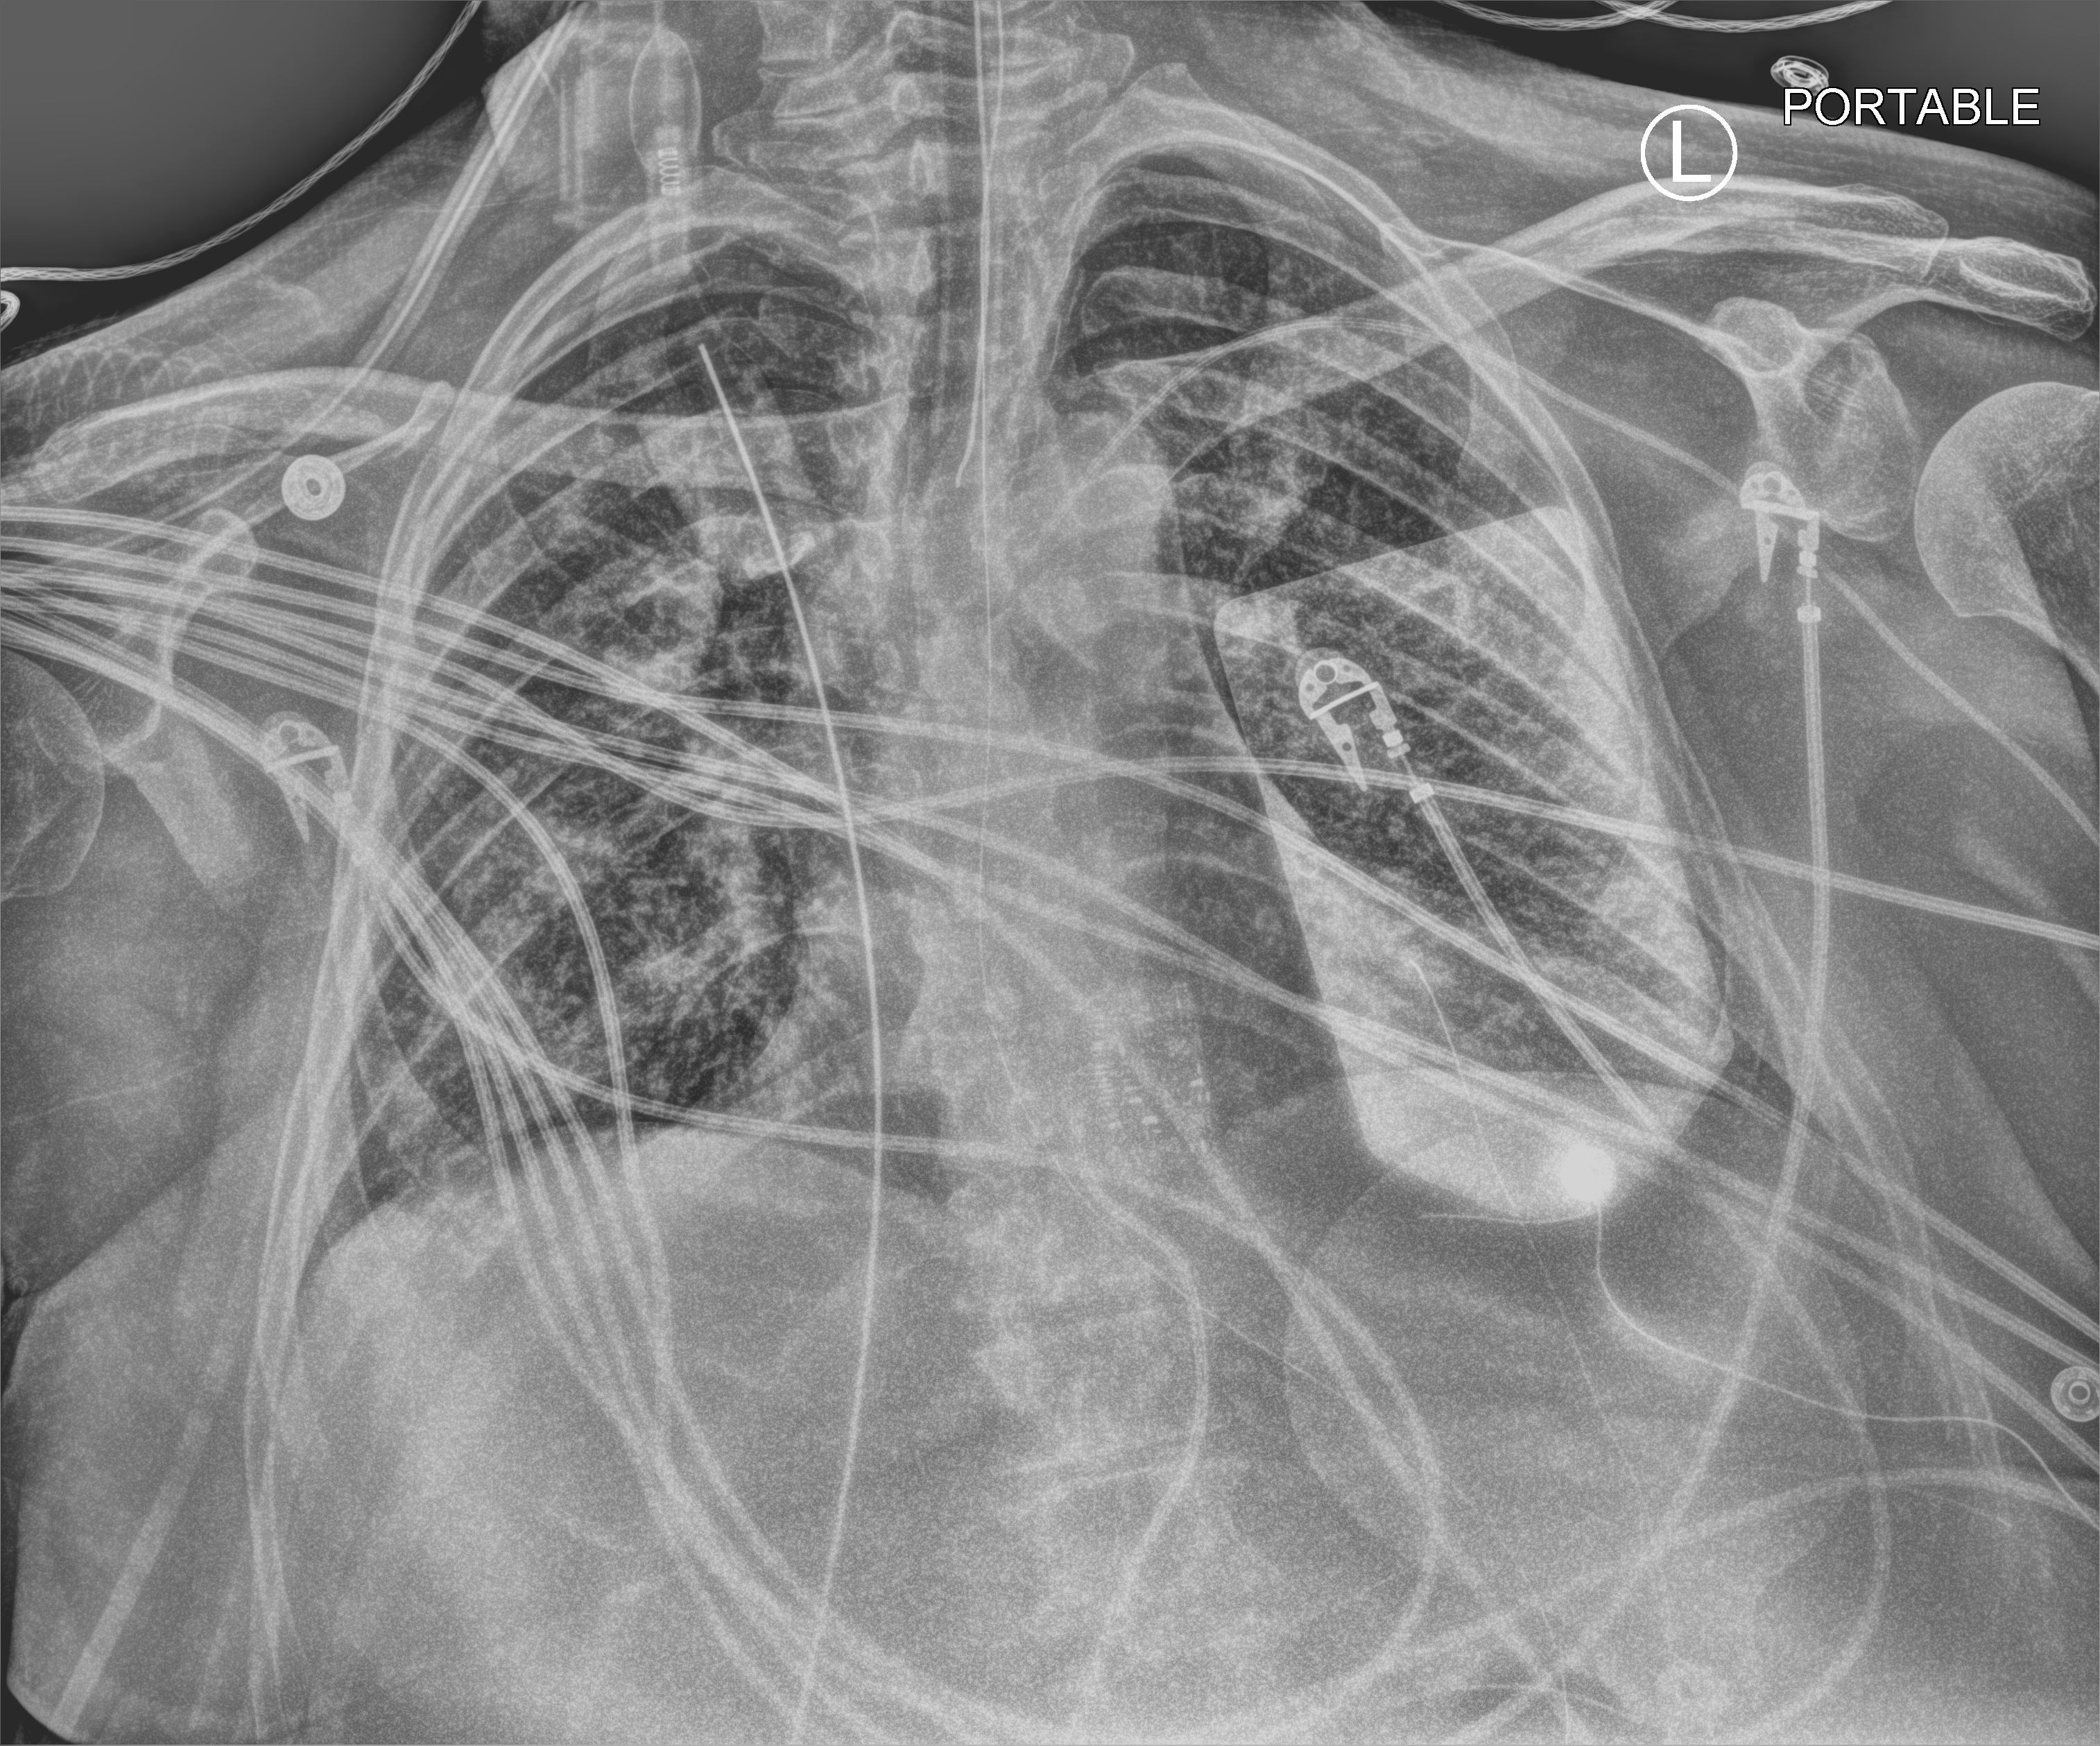
Bedside chest radiograph (computed radiography). Patient hospitalised with COVID-19; male, aged 18–59 years.
Hospital-stay facts (about this admission, not read from this image; timing relative to this image not recorded):
- admitted to intensive care during this hospital stay: yes
- length of hospital stay: 39 days
- mechanically ventilated during this hospital stay: yes